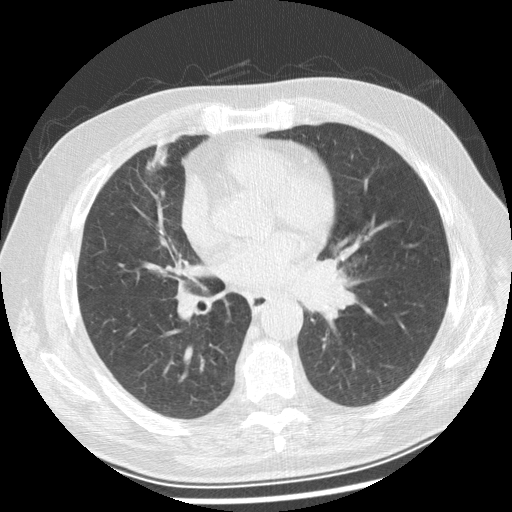
Chest CT (low-dose screening protocol), one axial image. Baseline screening round. Lung window (W 1500 / L -600 HU). 120 kVp. 512 × 512 image matrix. Male participant, aged 70 years at enrolment. Current smoker at enrolment.
Expert reader's lesion annotation, bounding box <293,240,377,324> (left, top, right, bottom; pixels). Screening reader's record for this exam: no non-calcified nodule ≥4 mm recorded. Official screen result: positive, change unspecified: nodule(s) >= 4 mm or enlarging nodule(s), mass(es), or other non-specific abnormalities suspicious for lung cancer. Later outcome: lung cancer diagnosed 29 days after this screen — squamous cell carcinoma, keratinizing, NOS, left main stem bronchus, moderately differentiated (G2), stage IIIB (AJCC 6th edition), 40 mm at pathology.